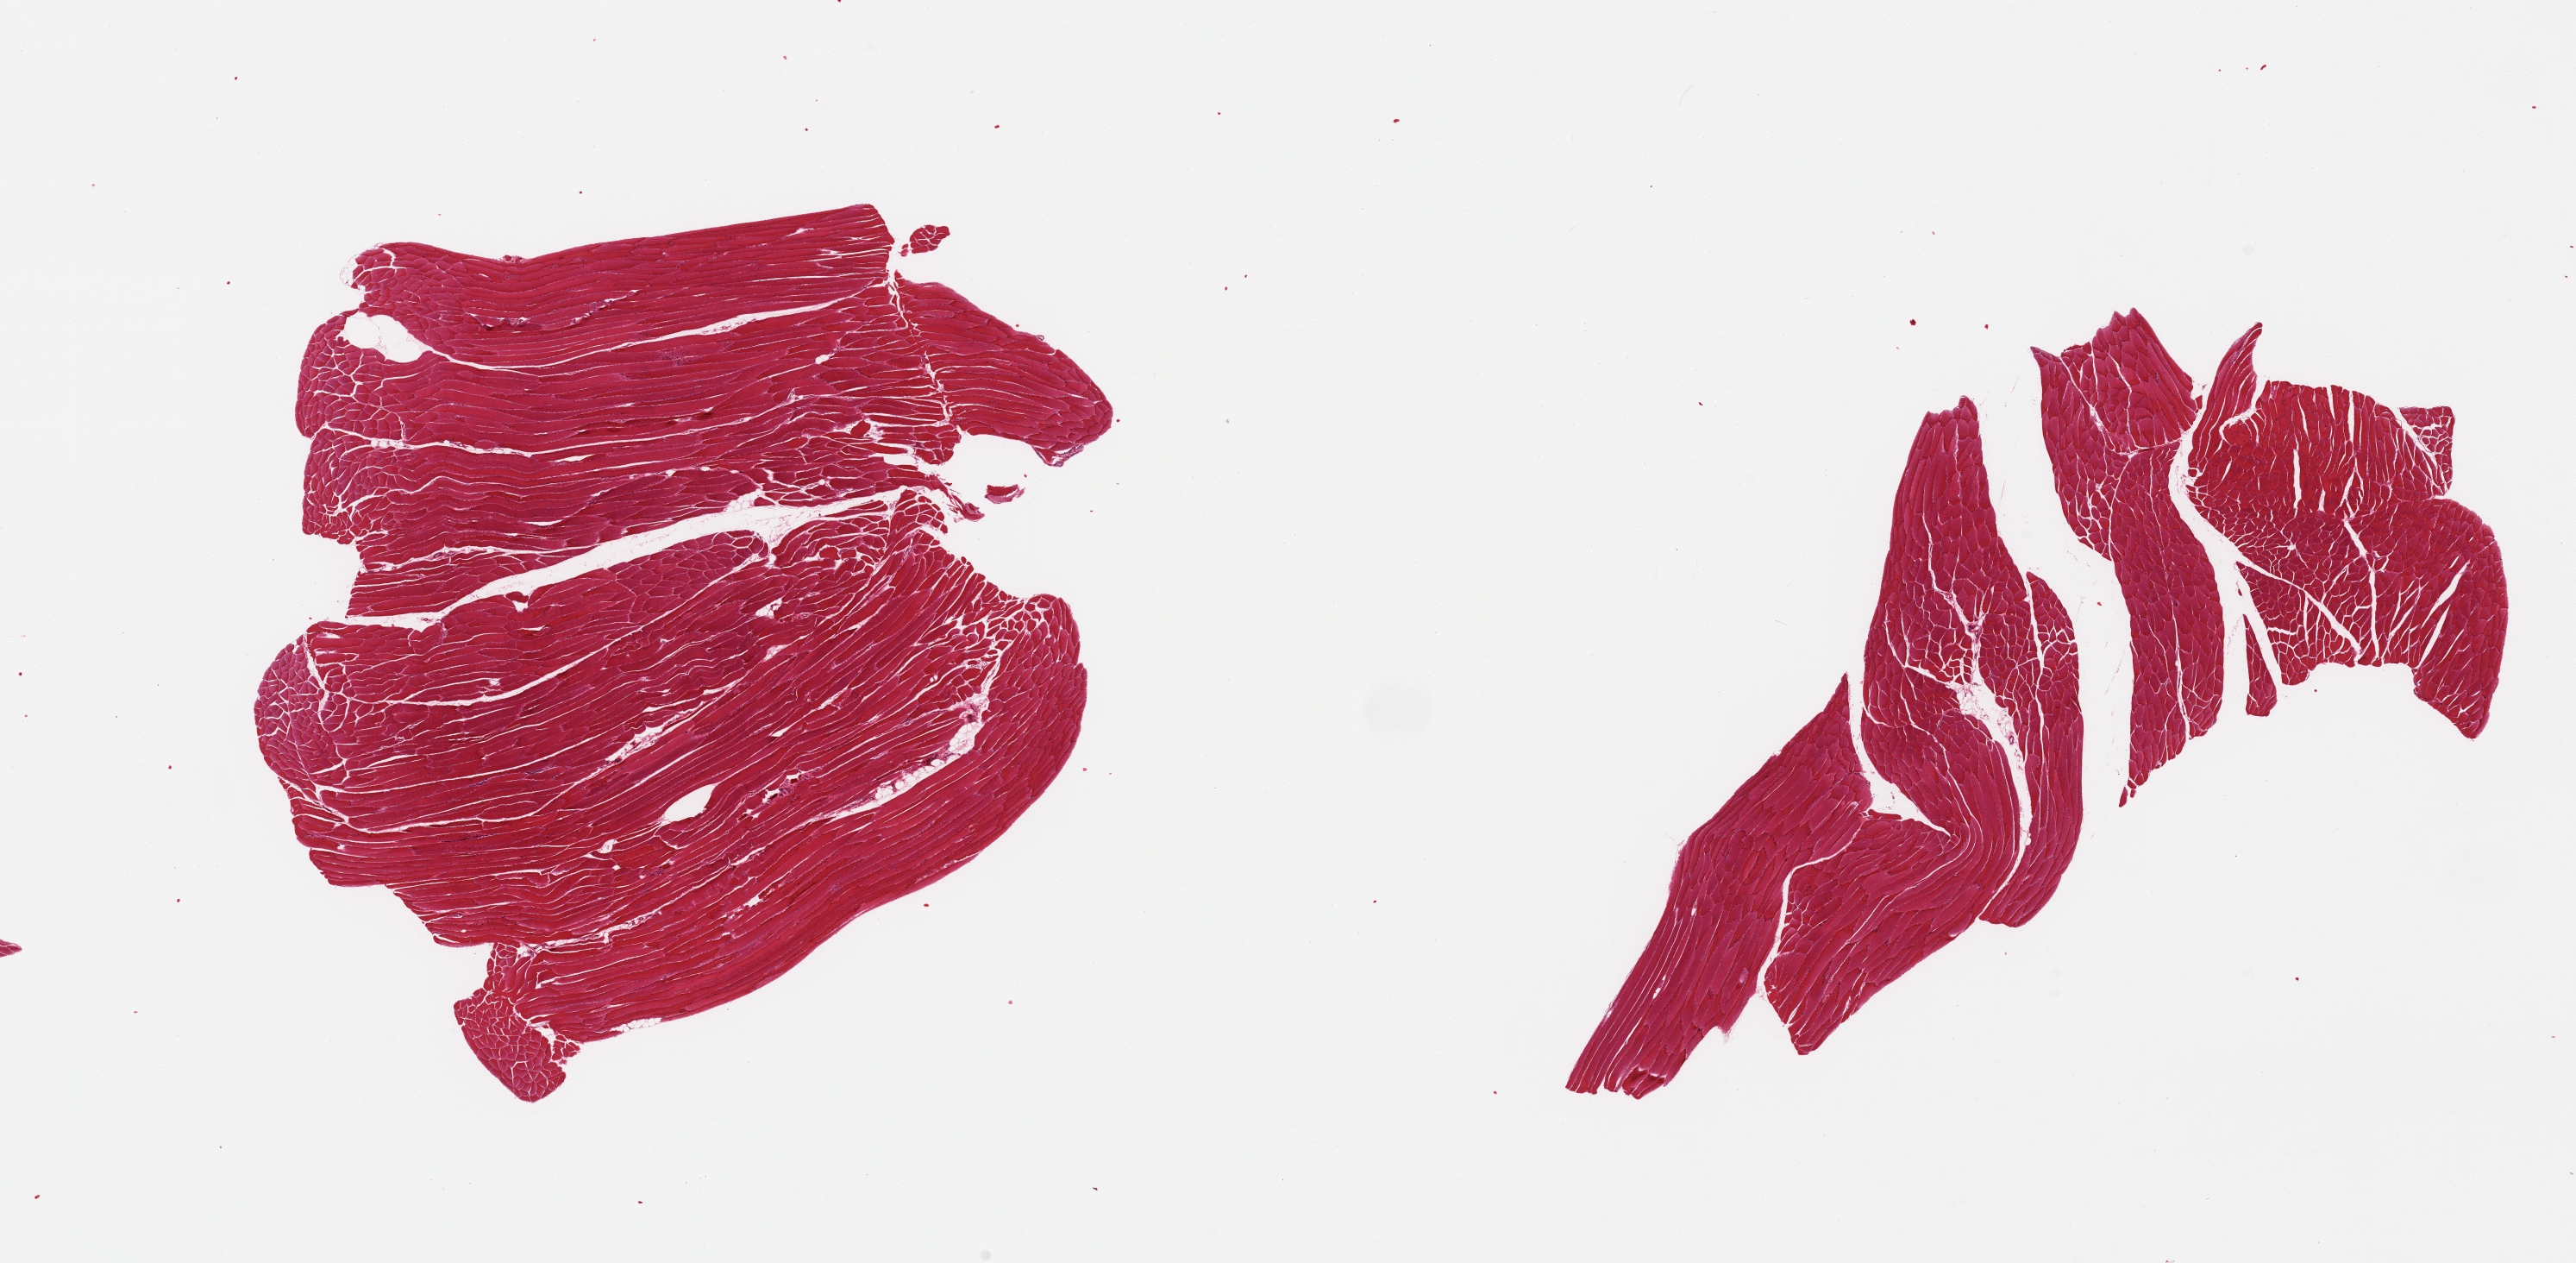
Digitized H&E-stained section — a low-resolution overview of the entire scanned area, about 23.6 x 11.6 mm. PAXgene-fixed paraffin-embedded (PFPE) section. Section of skeletal muscle (target tissue). Tissue donor sample. Male donor.
• review note (as recorded): 2 pieces